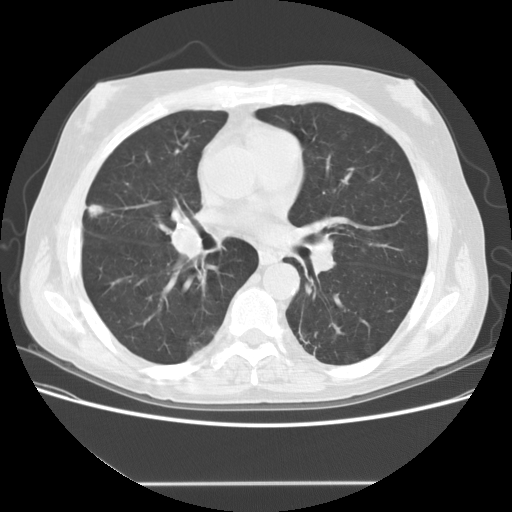
Low-dose screening chest CT, one axial slice; slice 87 of 153 in the series (ordered by position); lung window (W 1500 / L -600 HU); 2.5 mm slice thickness; 512 × 512 image matrix, field of view 360 × 360 mm.
Structures marked on this image (expert manual segmentation):
- lesion 2 (tumor, upper lobe of right lung): bounding box [x1, y1, x2, y2] px = [88, 204, 104, 217]